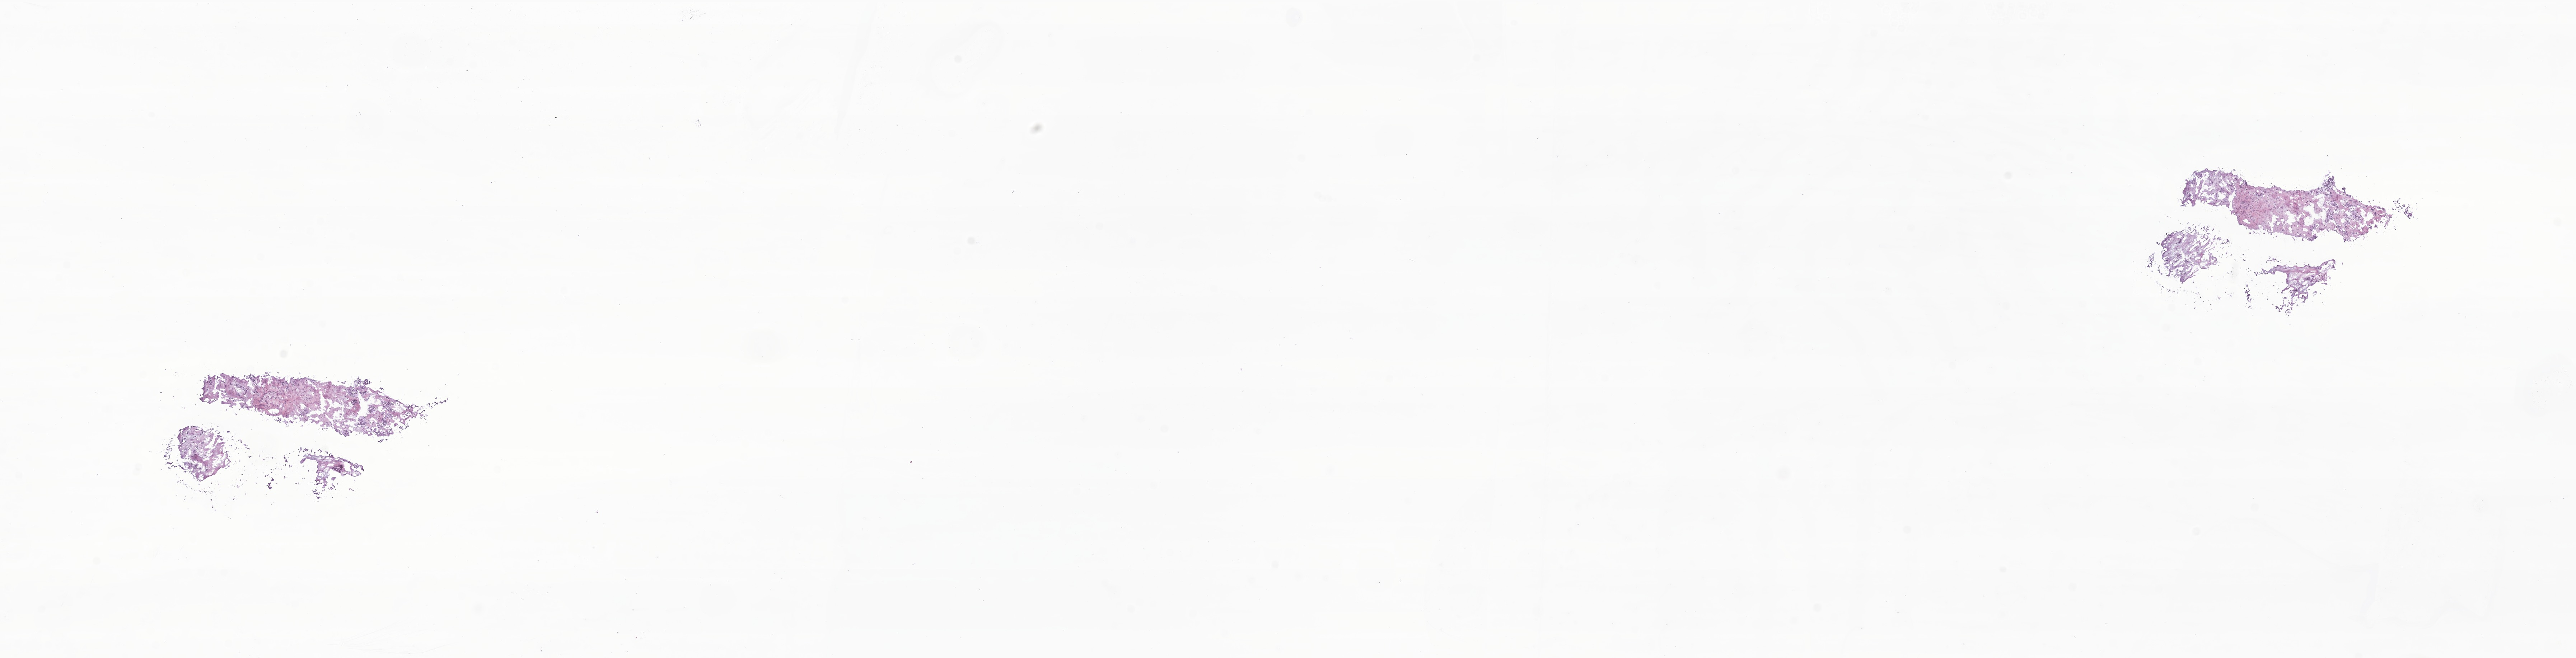
Digitized hematoxylin and eosin (H&E)-stained section of tumor tissue from the liver — low-resolution overview of the scanned area, about 30.3 x 7.7 mm; frozen section. Male patient, age 149 months (12 years 5 months).
- recorded diagnosis: Desmoplastic small round cell tumor